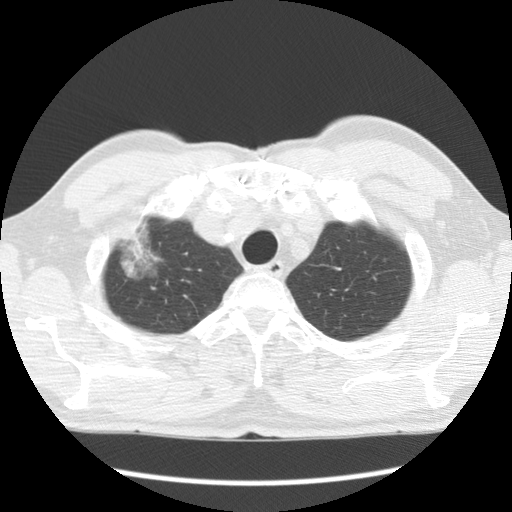
Low-dose screening chest CT, axial slice, first (baseline) screen, lung window (W 1500 / L -600 HU), standard (soft-tissue) reconstruction kernel (STANDARD), 512 × 512 image matrix, field of view 340 × 340 mm. Male participant, aged 64 years at enrolment.
Expert-annotated lung lesion, box from (x=107, y=216) to (x=171, y=282) px. The screening reader recorded 2 non-calcified nodules or masses ≥4 mm on this exam (right upper lobe, left upper lobe); which of them this box marks is not recorded.